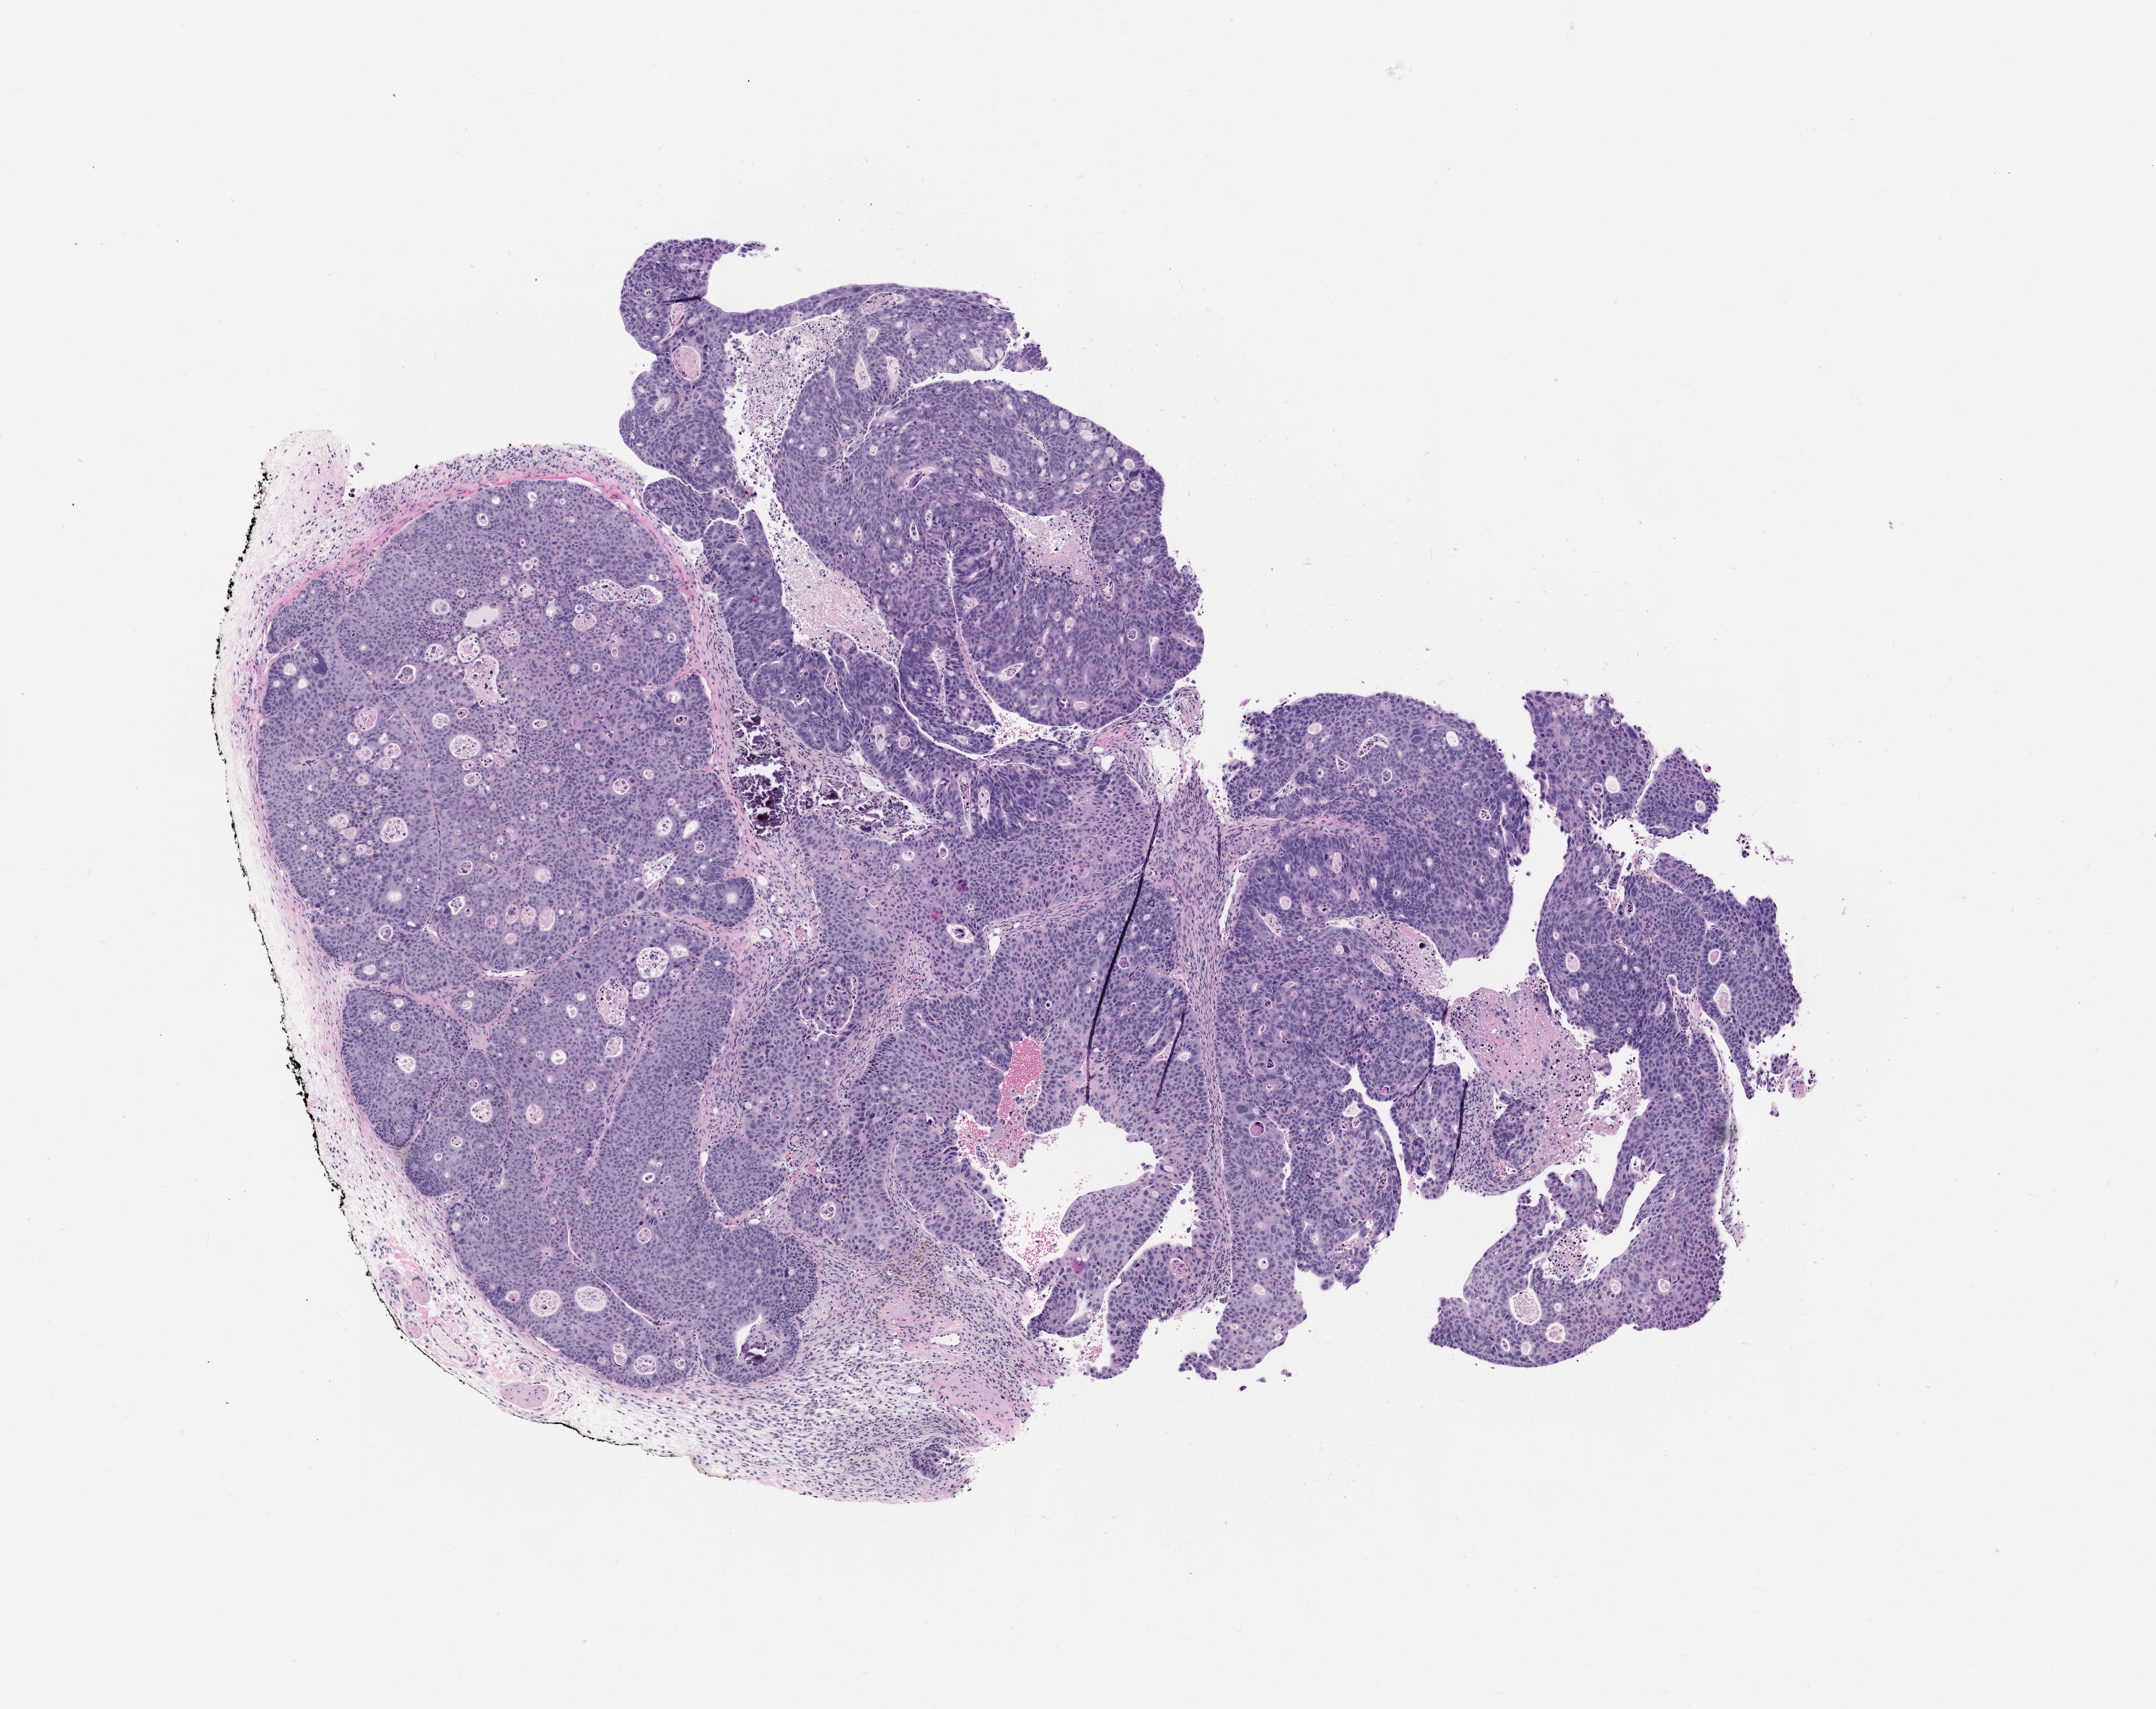
Whole-slide image, hematoxylin and eosin (H&E): patient-derived xenograft (human tumor grown in a mouse), passage 0 — a low-resolution overview of the entire scanned area, about 6.0 x 4.8 mm. Formalin-fixed, paraffin-embedded (FFPE) tissue. Tumor site category: colon.
Originating patient diagnosis: Colon Adenocarcinoma.